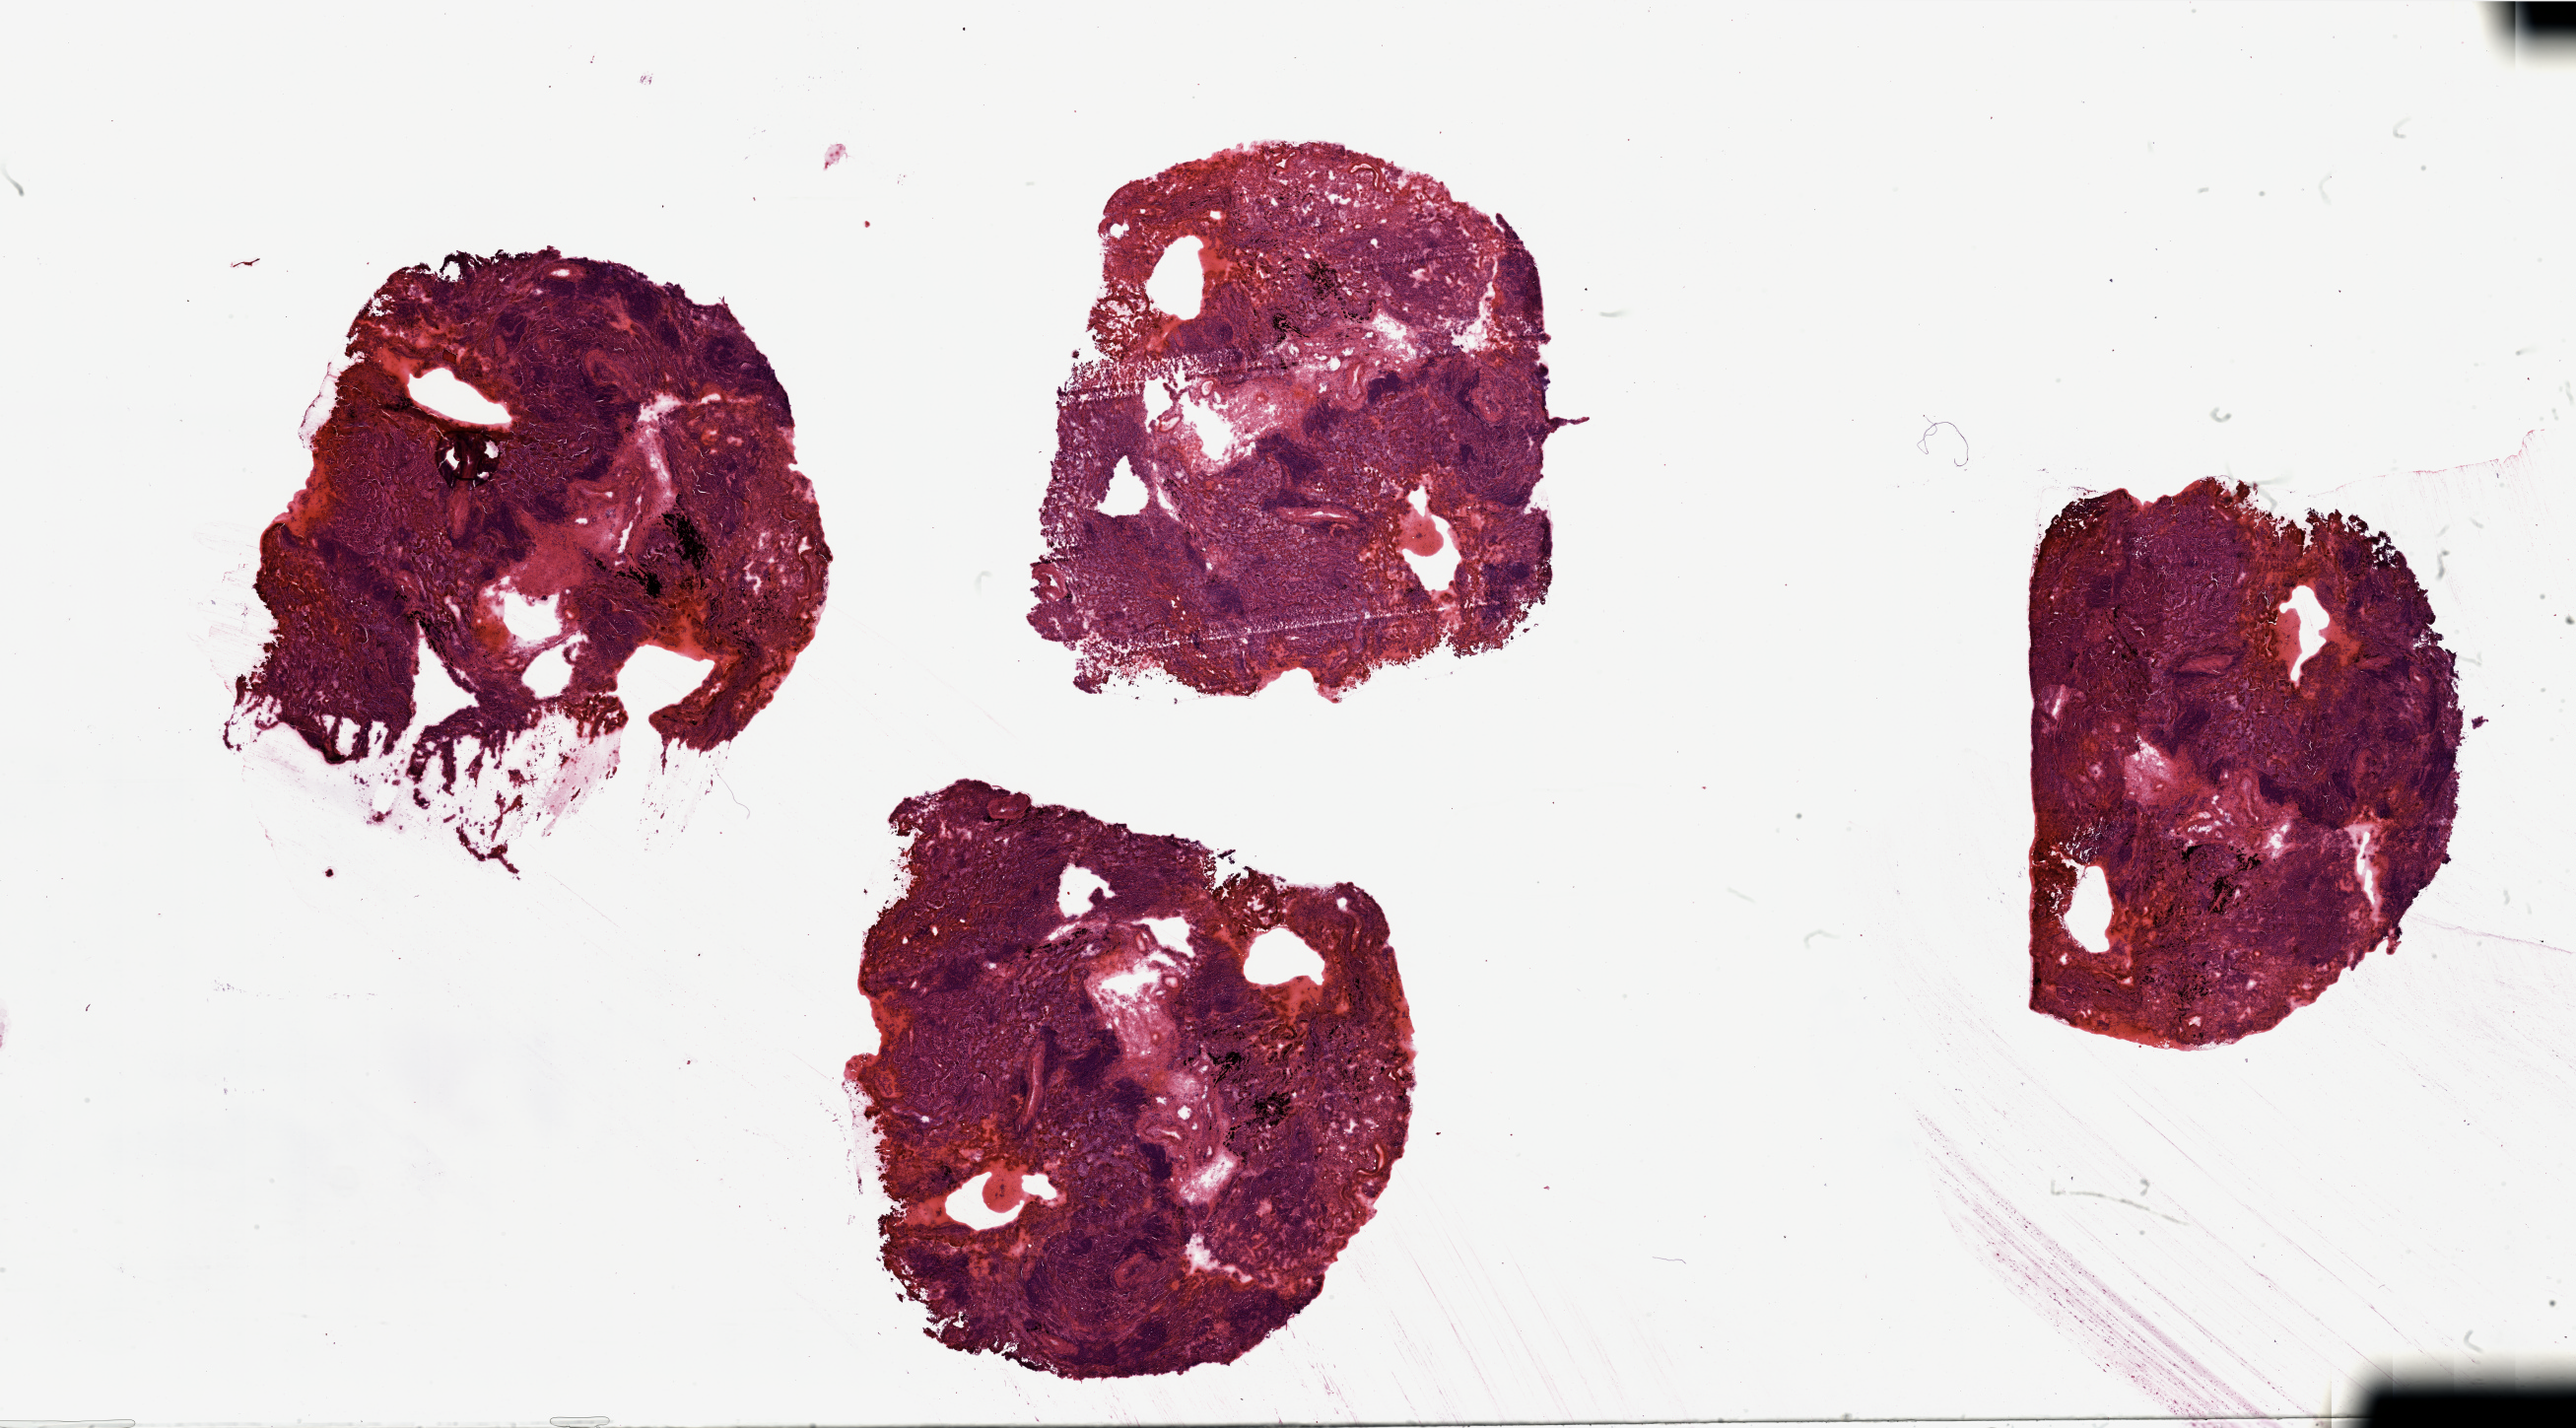
Whole-slide histology image, H&E-stained, shown as a low-resolution overview of the whole scanned area (about 41.3 x 22.9 mm); tumour tissue sample, sampled site: lung. Patient: male, age 73 years. Histologic grade: GX (grade cannot be assessed). Pathologist review of this section (percent, as recorded): tumour nuclei 60%, necrosis 10%.
Primary tumour site (as recorded): right upper lobe. Diagnosis: Adenocarcinoma, NOS. AJCC pathologic stage: IB.